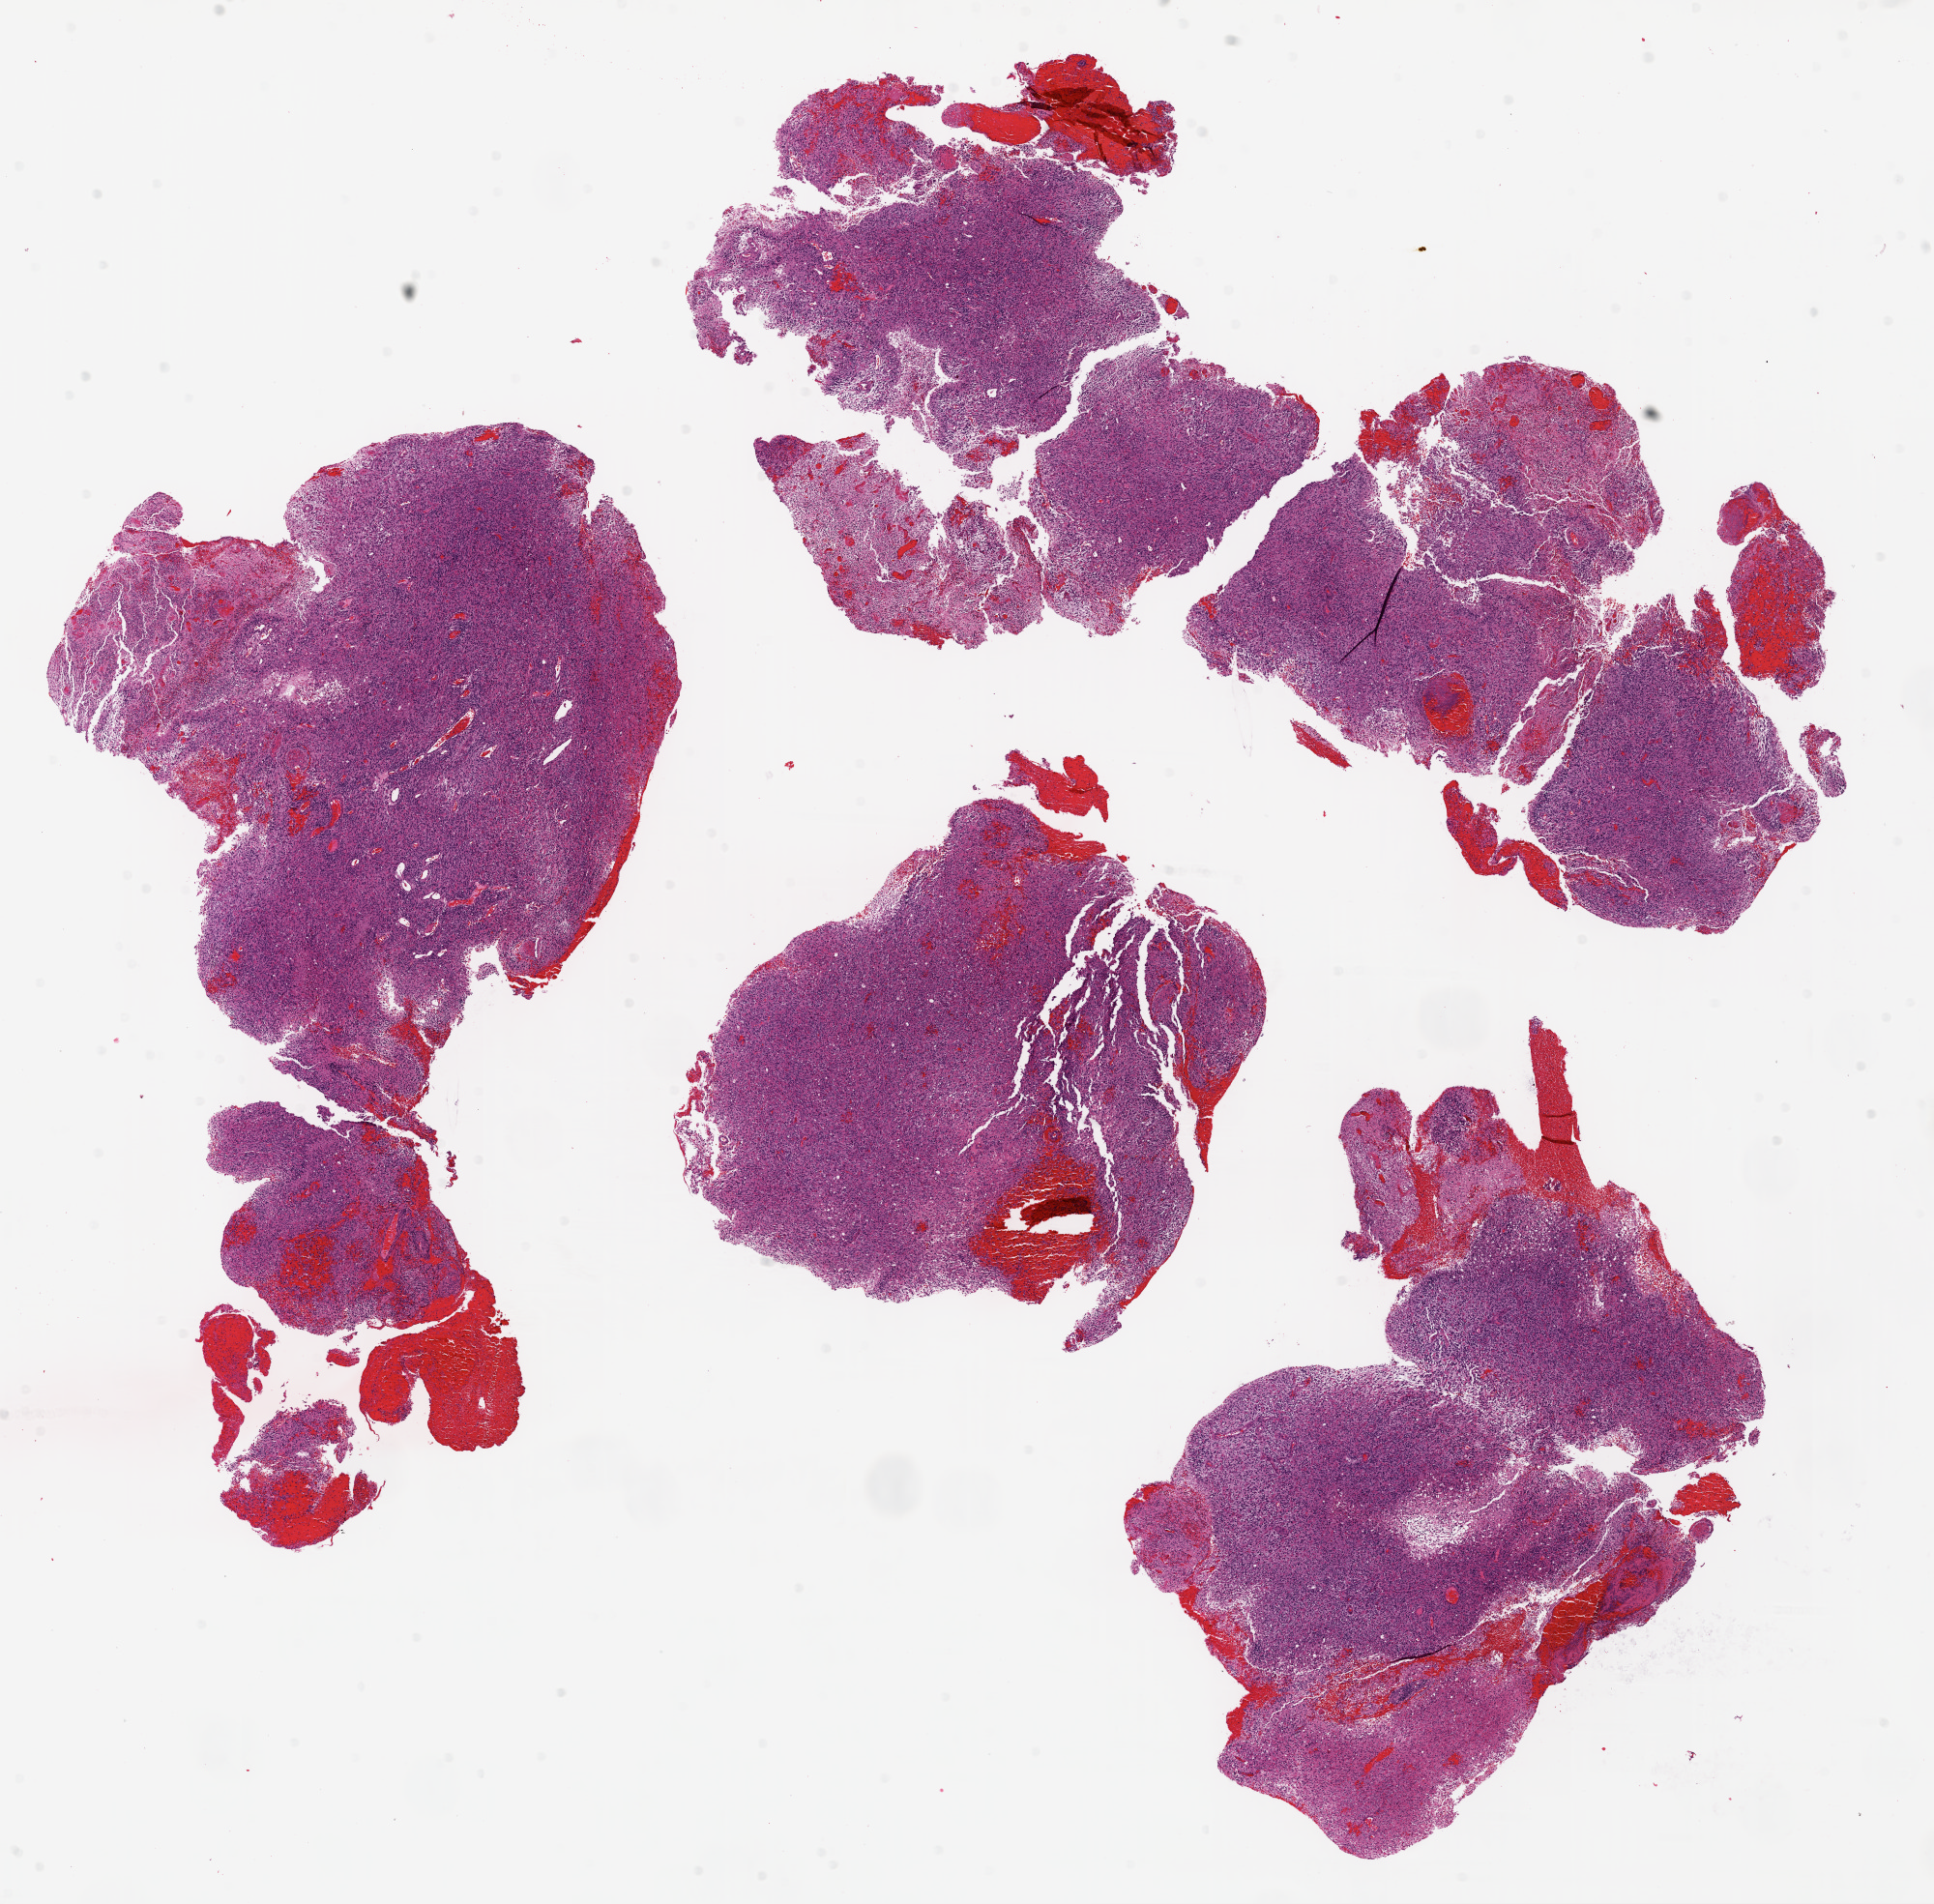
Digitized Hematoxylin and eosin (H&E) stained tissue section (whole slide) — shown as a low-resolution overview of the whole scanned area (about 16.0 x 15.8 mm, acquisition: 20x scan). FFPE section. Brain, primary tumour sample. Female, age 40 years at initial diagnosis.
- pathologic diagnosis: Glioblastoma